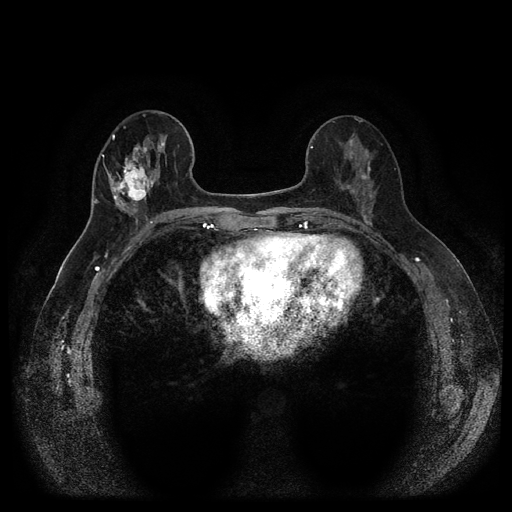
Breast MRI (dynamic contrast-enhanced, multi-phase), one axial slice; dynamic contrast-enhanced series, time point 2 of 5 at this slice position (early post-contrast); 1.5 T; TE 2.6 ms, TR 5.4 ms; 2 mm slice thickness; 512 × 512 image matrix. Patient: female, 56 years.
Outlined on this slice (semi-automatically segmented with operator editing):
- breast lesion (labelled 'tumour' in the annotation; benign lesions carry a separate 'benign' label): box from (x=108, y=152) to (x=159, y=211) px